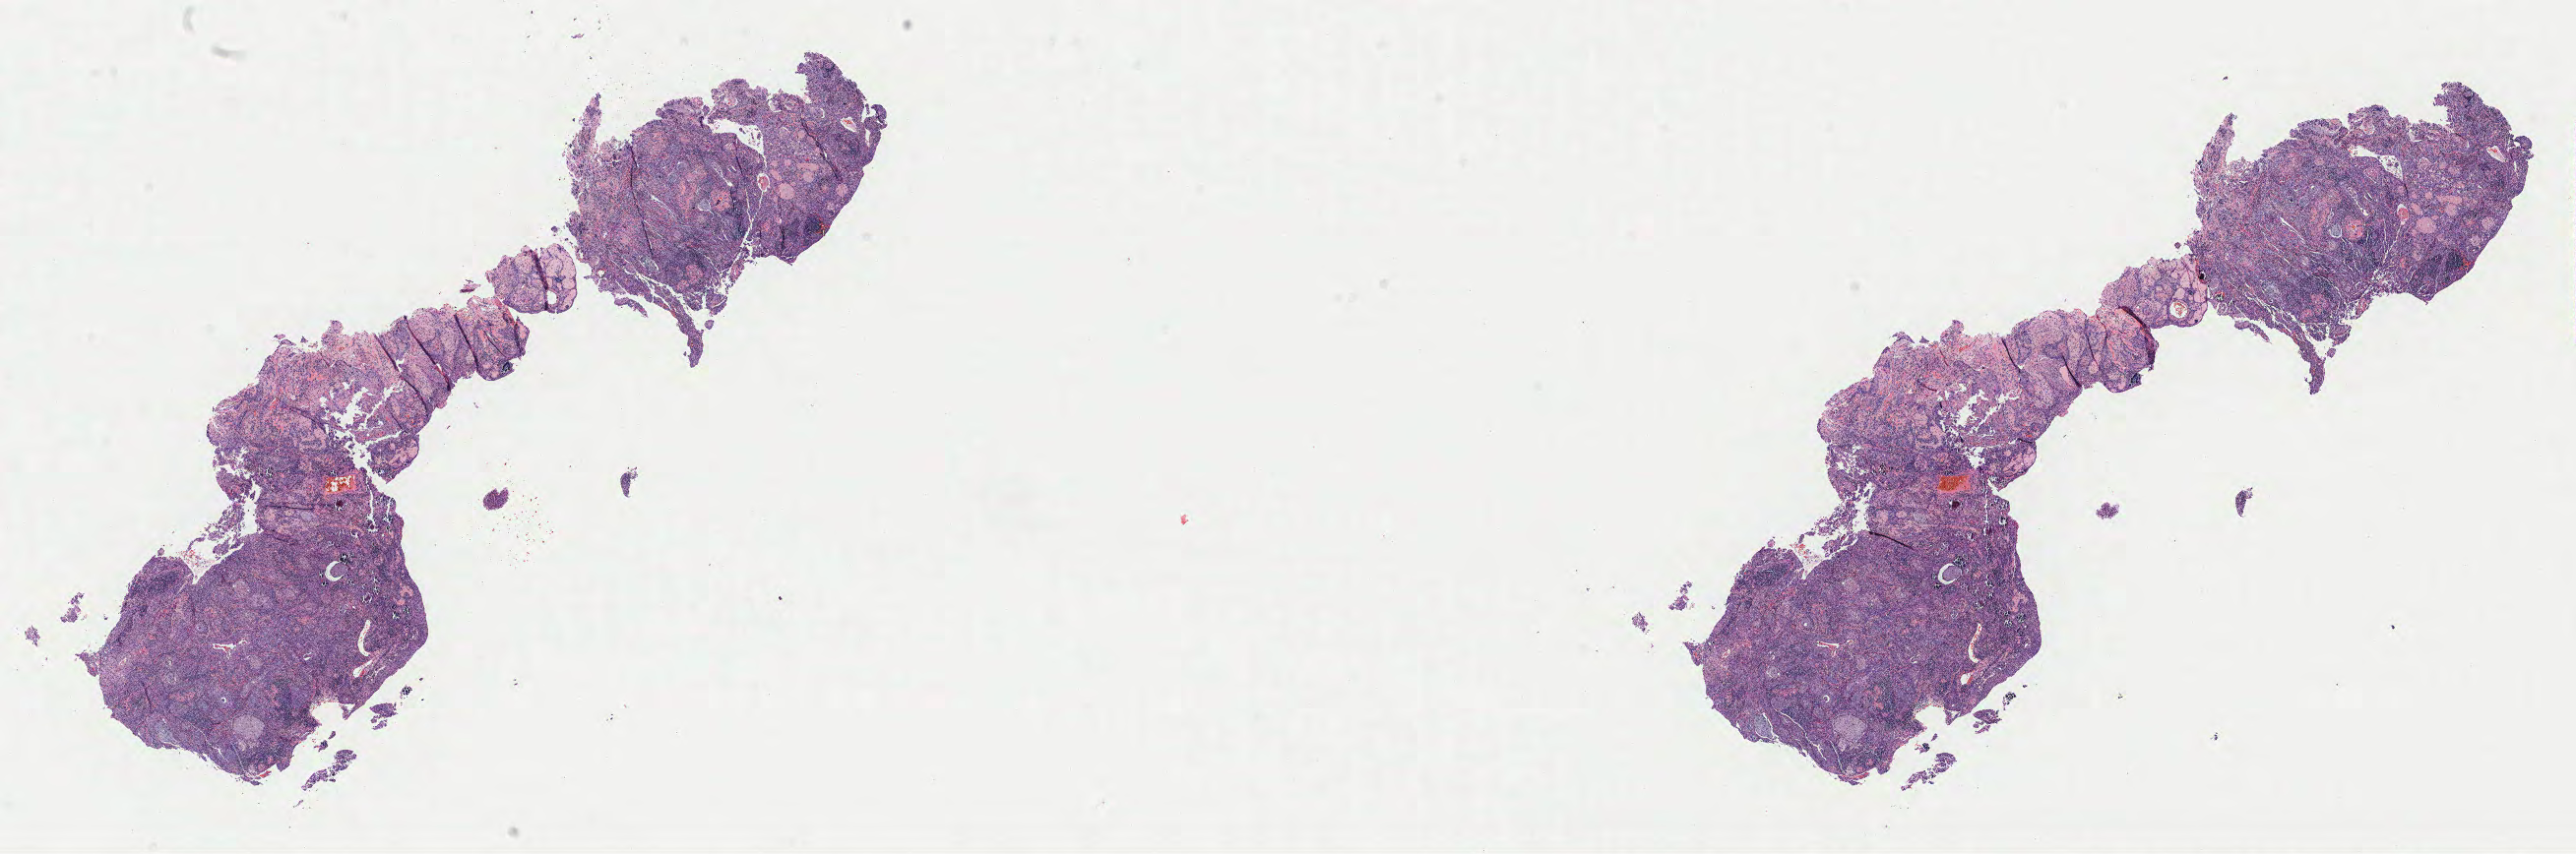
Digitized hematoxylin and eosin (H&E)-stained section — a low-resolution overview of the entire scanned area, about 20.8 x 6.9 mm, specimen: tumor tissue, anatomic site: cervix. Patient female; 60 years old.
• diagnosis: Squamous cell carcinoma, keratinizing, NOS